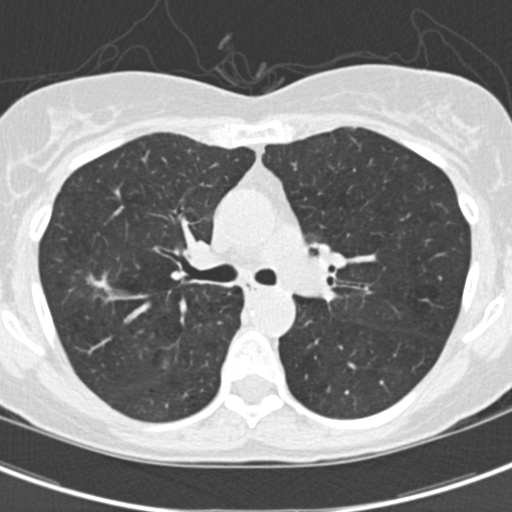
Low-dose screening chest CT, one axial slice. Position 99 of 154 along the scan axis. Reconstruction kernel B30f. 120 kVp. Lung window (W 1500 / L -600 HU). 2 mm slice thickness. 512 × 512 image matrix.
Outlined on this slice (outlined manually by an expert reader):
- lesion 1 (tumor, upper lobe of right lung): bounding box <87,273,111,293> (left, top, right, bottom; pixels)